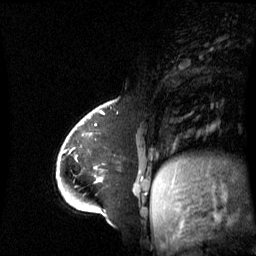
Breast MRI (dynamic contrast-enhanced), one sagittal slice; position 18 of 60 along the scan axis; dynamic contrast-enhanced series, image 2 of 3 at this slice position (ordered by acquisition); 1.5 T; TE 4.2 ms, TR 8.4 ms; 2.8 mm slice thickness; 256 × 256 image matrix, field of view 270 × 270 mm. Female patient, age 43 years. From the clinical record (not read from this slice): setting: breast cancer imaged before/during neoadjuvant chemotherapy; receptor status: triple-negative.
Annotated regions visible in this slice (semi-automatically segmented with operator editing):
- analysis volume of interest (the breast-tissue region the enhancement analysis was run in; not a lesion): bounding box (x1, y1, x2, y2) in pixels: (65, 118, 143, 198)
- tumour enhancement mask (voxels above the 70 % enhancement threshold inside the analysis volume of interest): (65, 150, 102, 181)